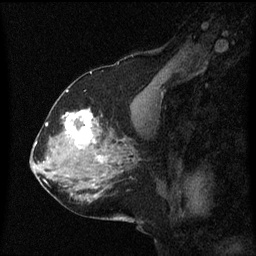
Breast MRI (dynamic contrast-enhanced), one sagittal slice. Dynamic contrast-enhanced series, image 2 of 3 at this slice position (ordered by acquisition). 1.5 T. TE 4.2 ms, TR 8.4 ms. 2 mm slice thickness. 256 × 256 image matrix, field of view 200 × 200 mm. Patient: female, 58 years.
Annotated regions visible in this slice (semi-automatically segmented with operator editing):
- analysis volume of interest (the breast-tissue region the enhancement analysis was run in; not a lesion): bounding box <58,108,99,151> (left, top, right, bottom; pixels)
- tumour enhancement mask (voxels above the 70 % enhancement threshold inside the analysis volume of interest): <64,110,97,145>